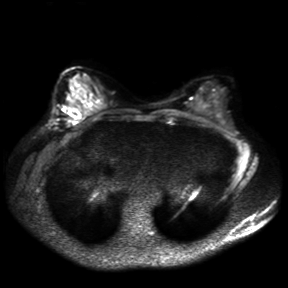
Breast MRI, one axial slice; slice 18 of 30 in the series (ordered by position); diffusion-weighted series; image 2 of 4 stored at this slice position (different b-values; order by instance number); 3 T; 4 mm slice thickness; 288 × 288 image matrix, field of view 360 × 360 mm. Female patient.
Annotated regions visible in this slice (expert manual segmentation):
- tumour on diffusion-weighted imaging: box from (x=67, y=108) to (x=80, y=120) px